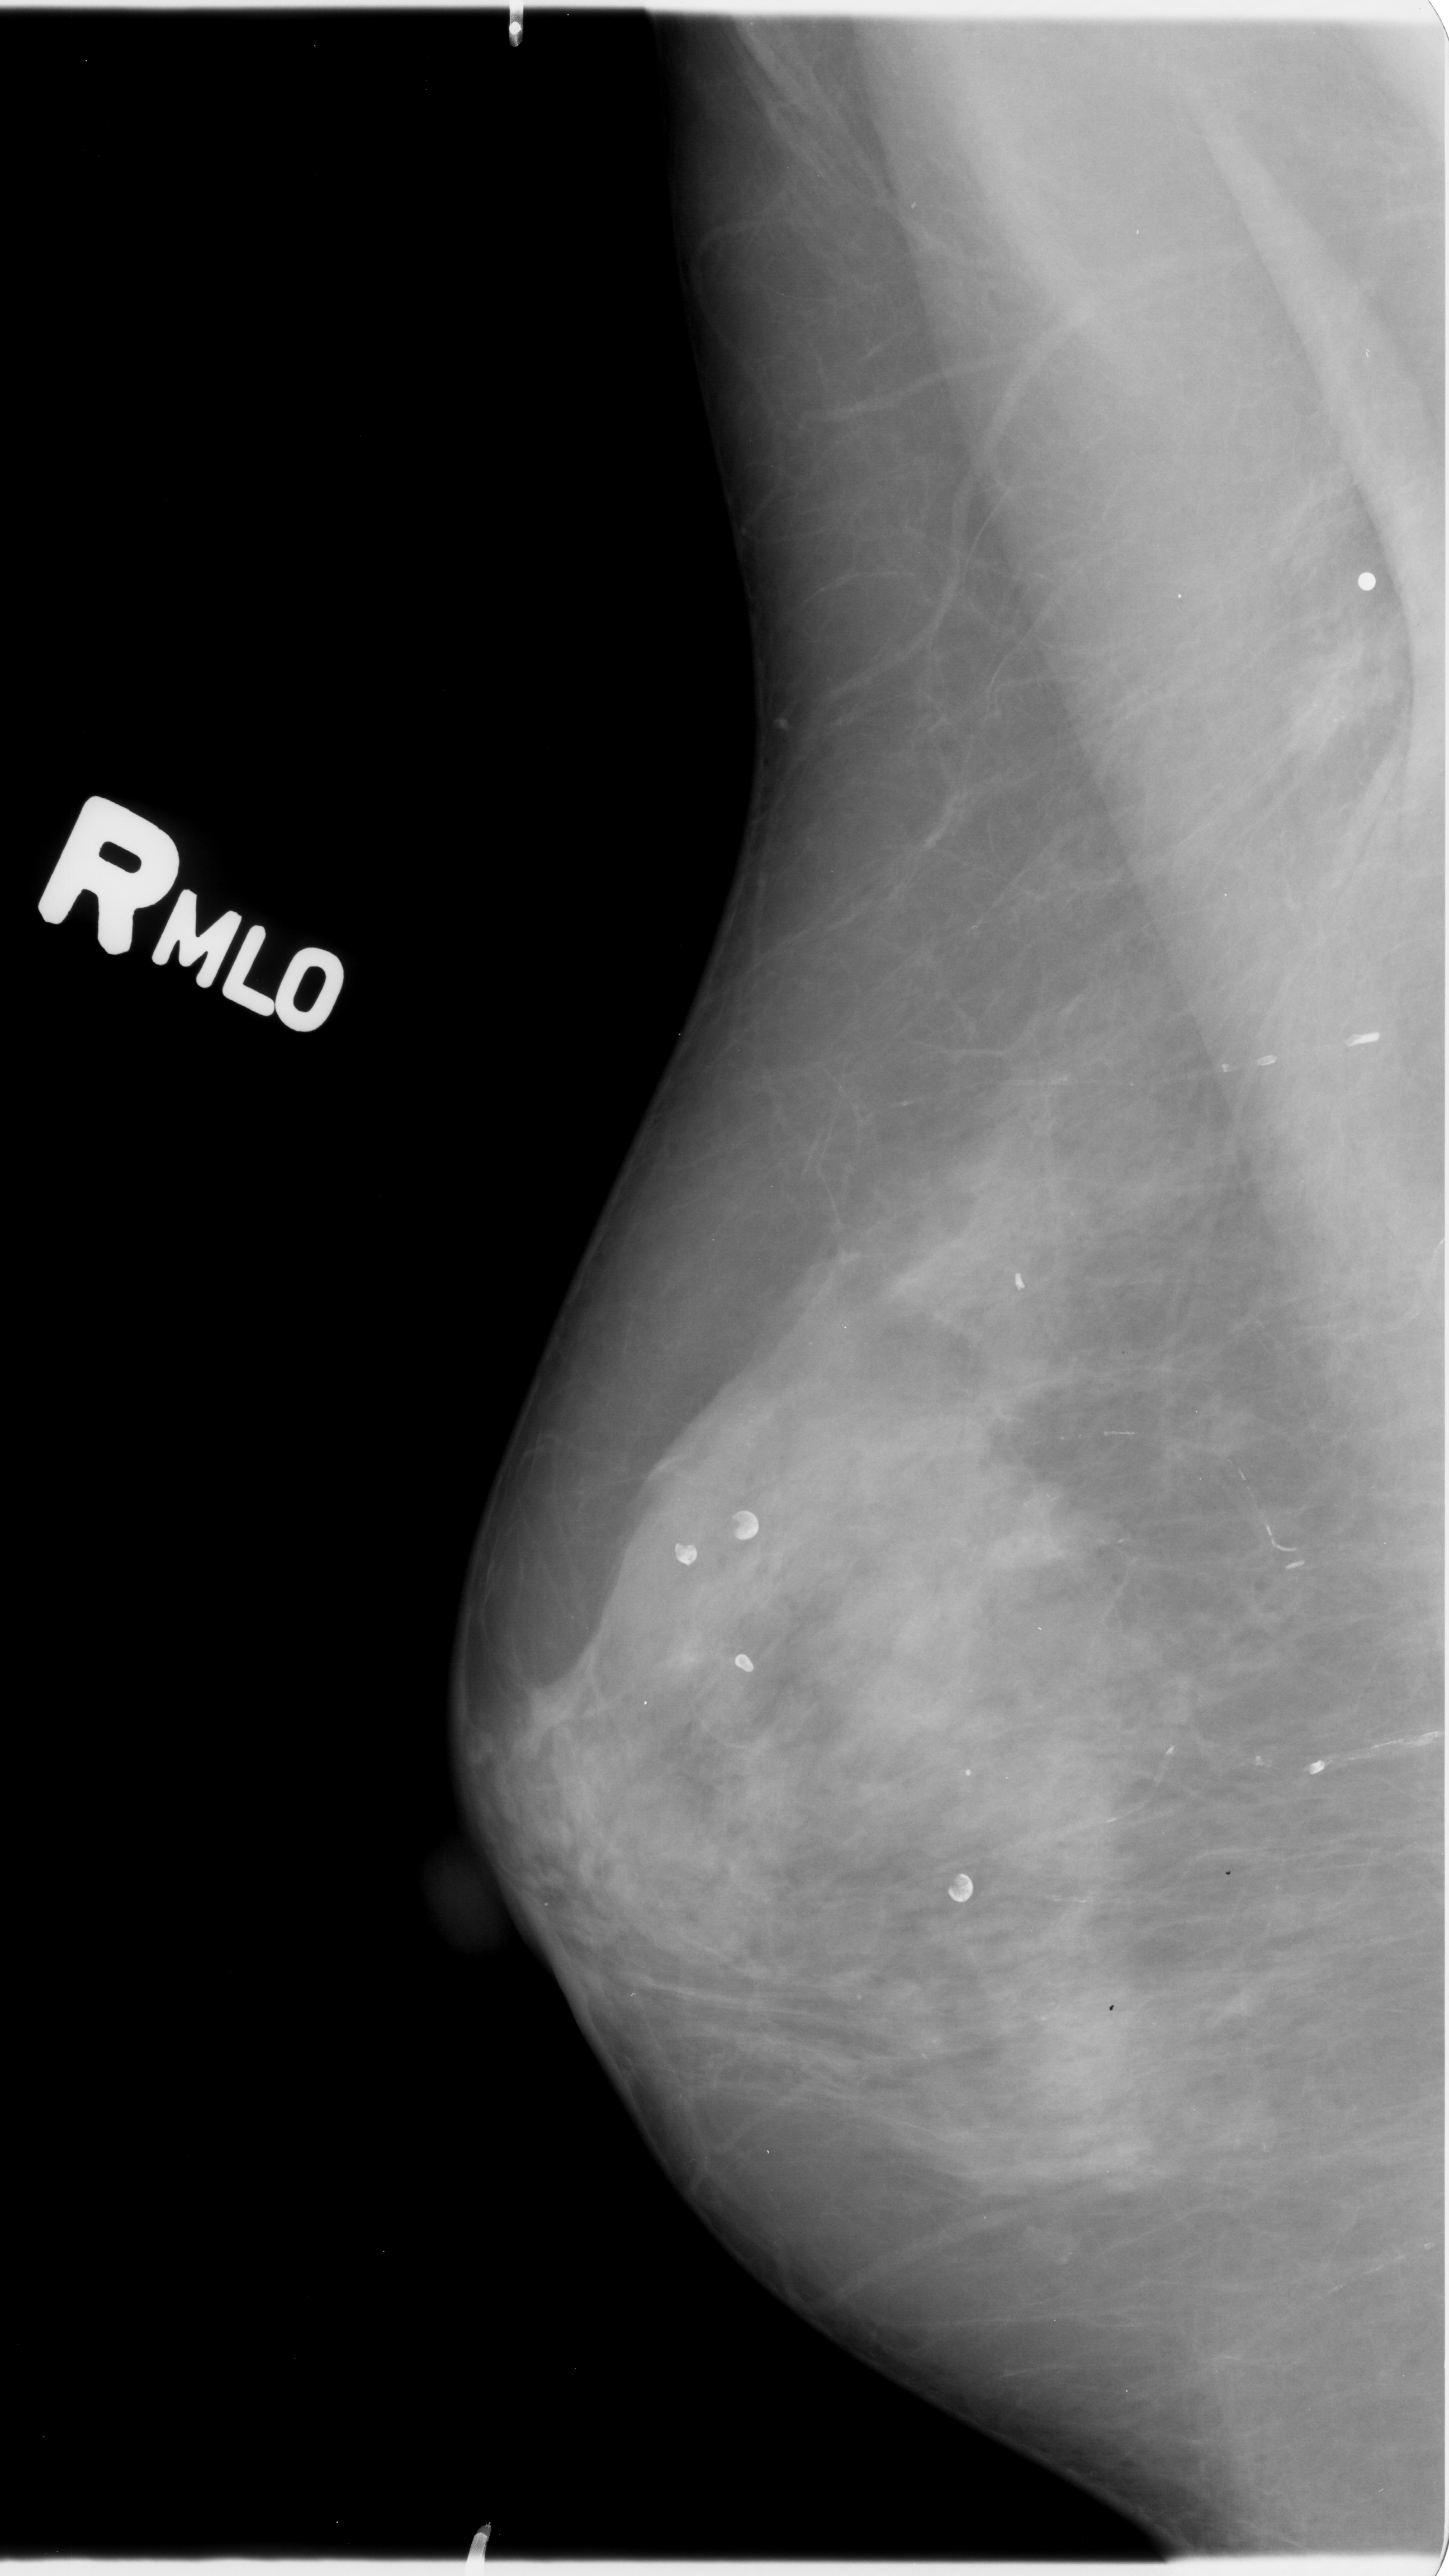
Digitized screen-film mammogram; right breast; MLO view; breast composition: heterogeneously dense (BI-RADS density category 3 of 4).
- Radiologist-marked abnormalities on this image: mass, shape irregular, margins spiculated; BI-RADS assessment category 4; pathology (as recorded): malignant.